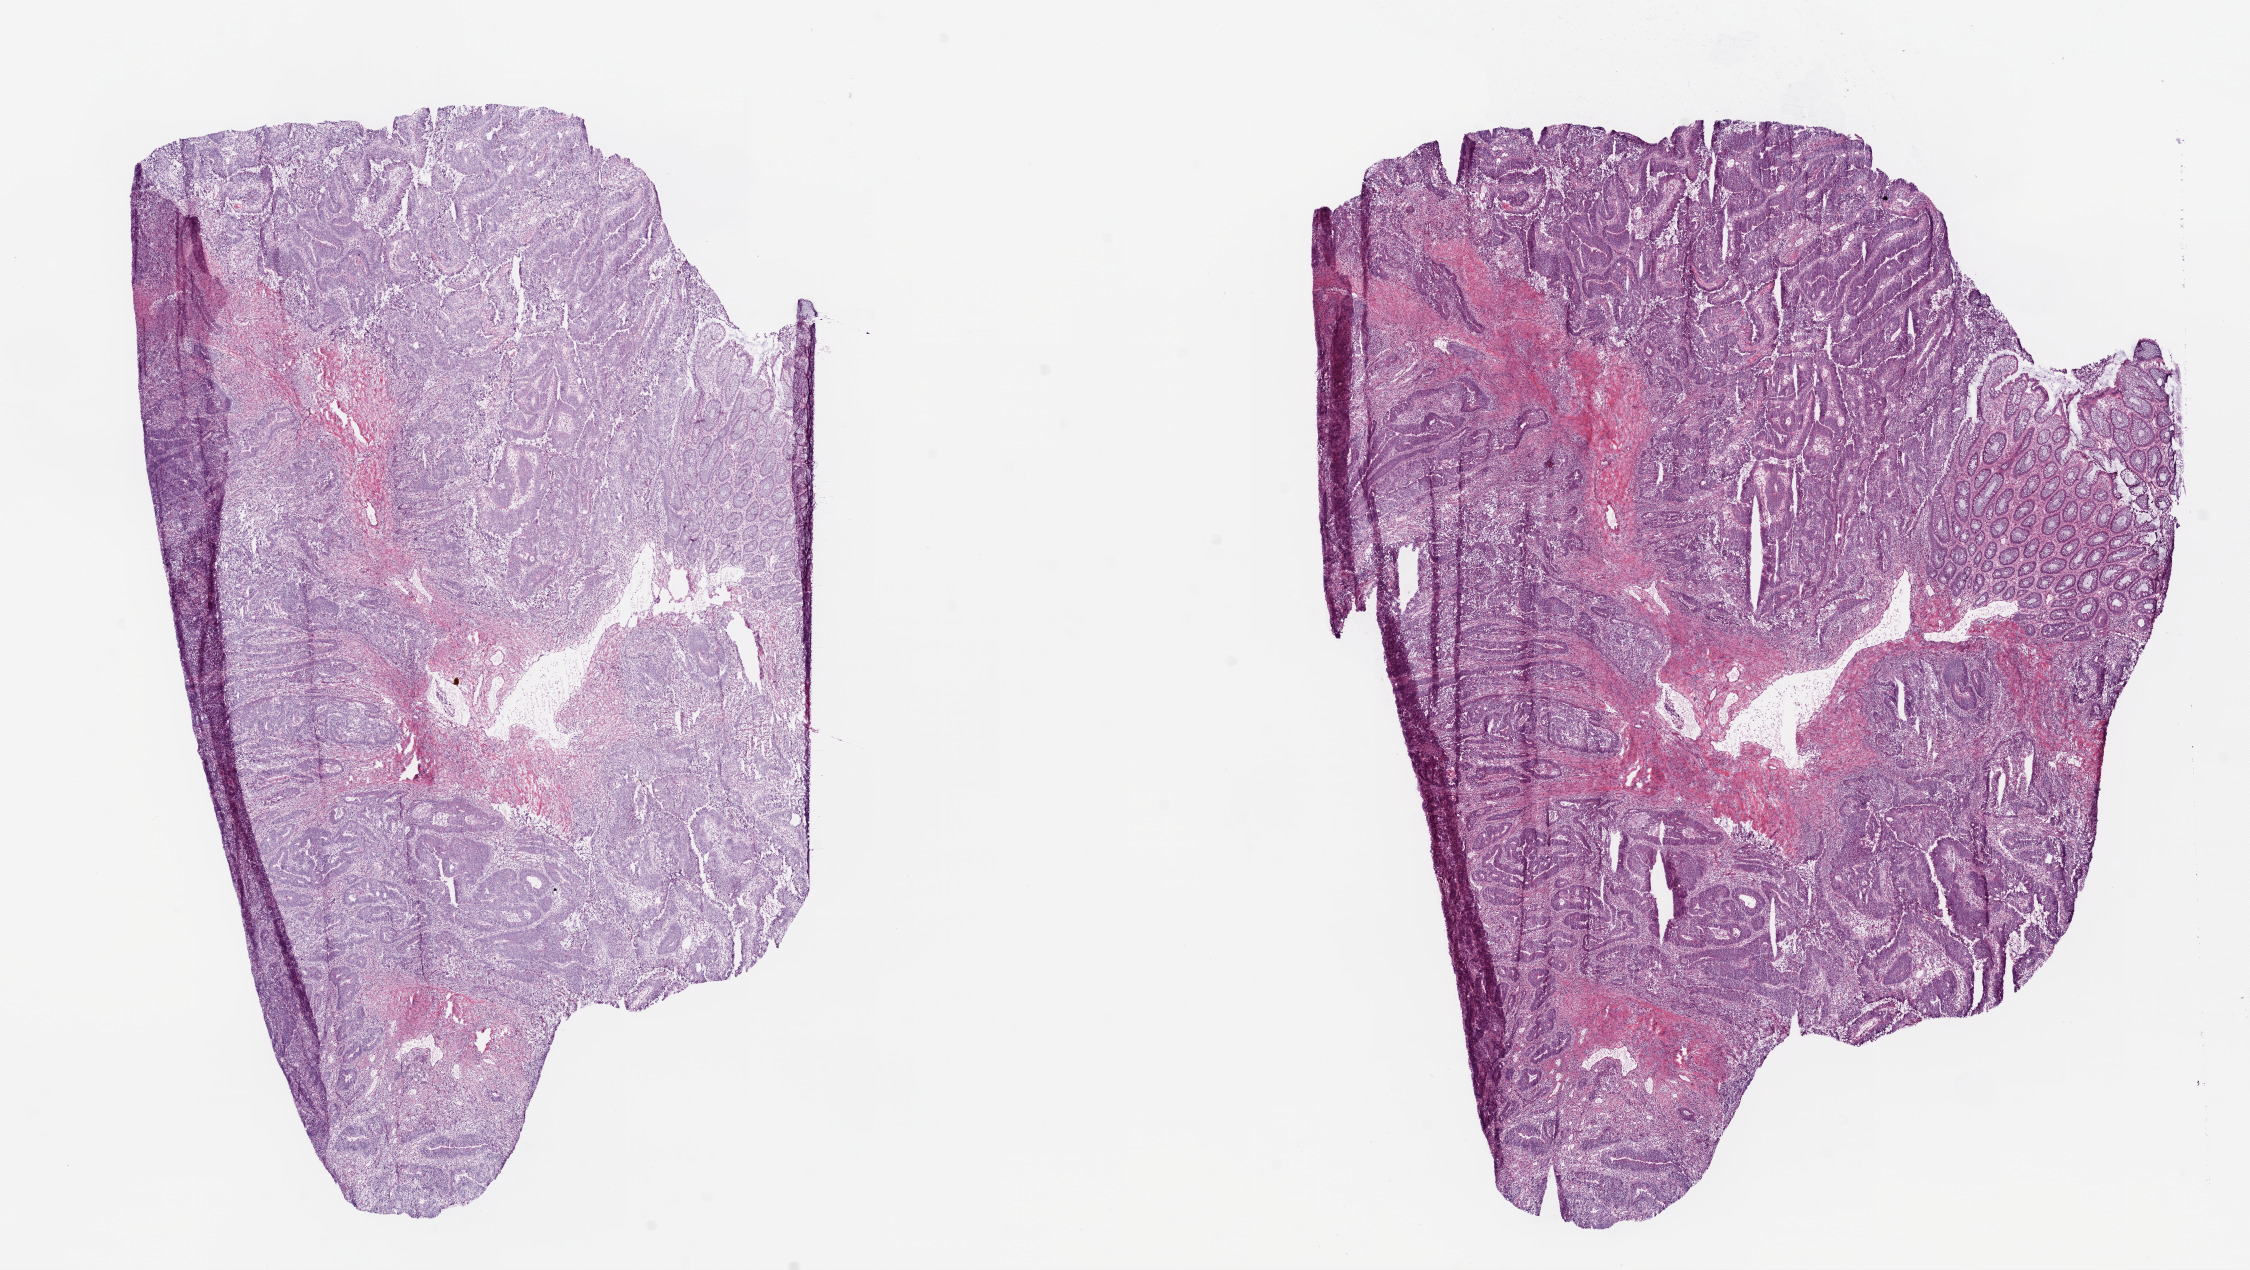
H&E-stained whole-slide image — shown as a low-resolution overview of the whole scanned area (about 18.1 x 10.2 mm), frozen section, sample: primary tumour, colon. Female patient. Pathologist review of this section (percent, as recorded): tumour cells 80%, tumour nuclei 80%, normal cells 7%, stromal cells 13%, necrosis 0%. Infiltration values recorded for this section: lymphocyte infiltration 5%, neutrophil infiltration 1%.
Histologic diagnosis: Adenocarcinoma, NOS. AJCC pathologic stage: I. Lymph nodes positive (case pathology): 0 of 19 examined.